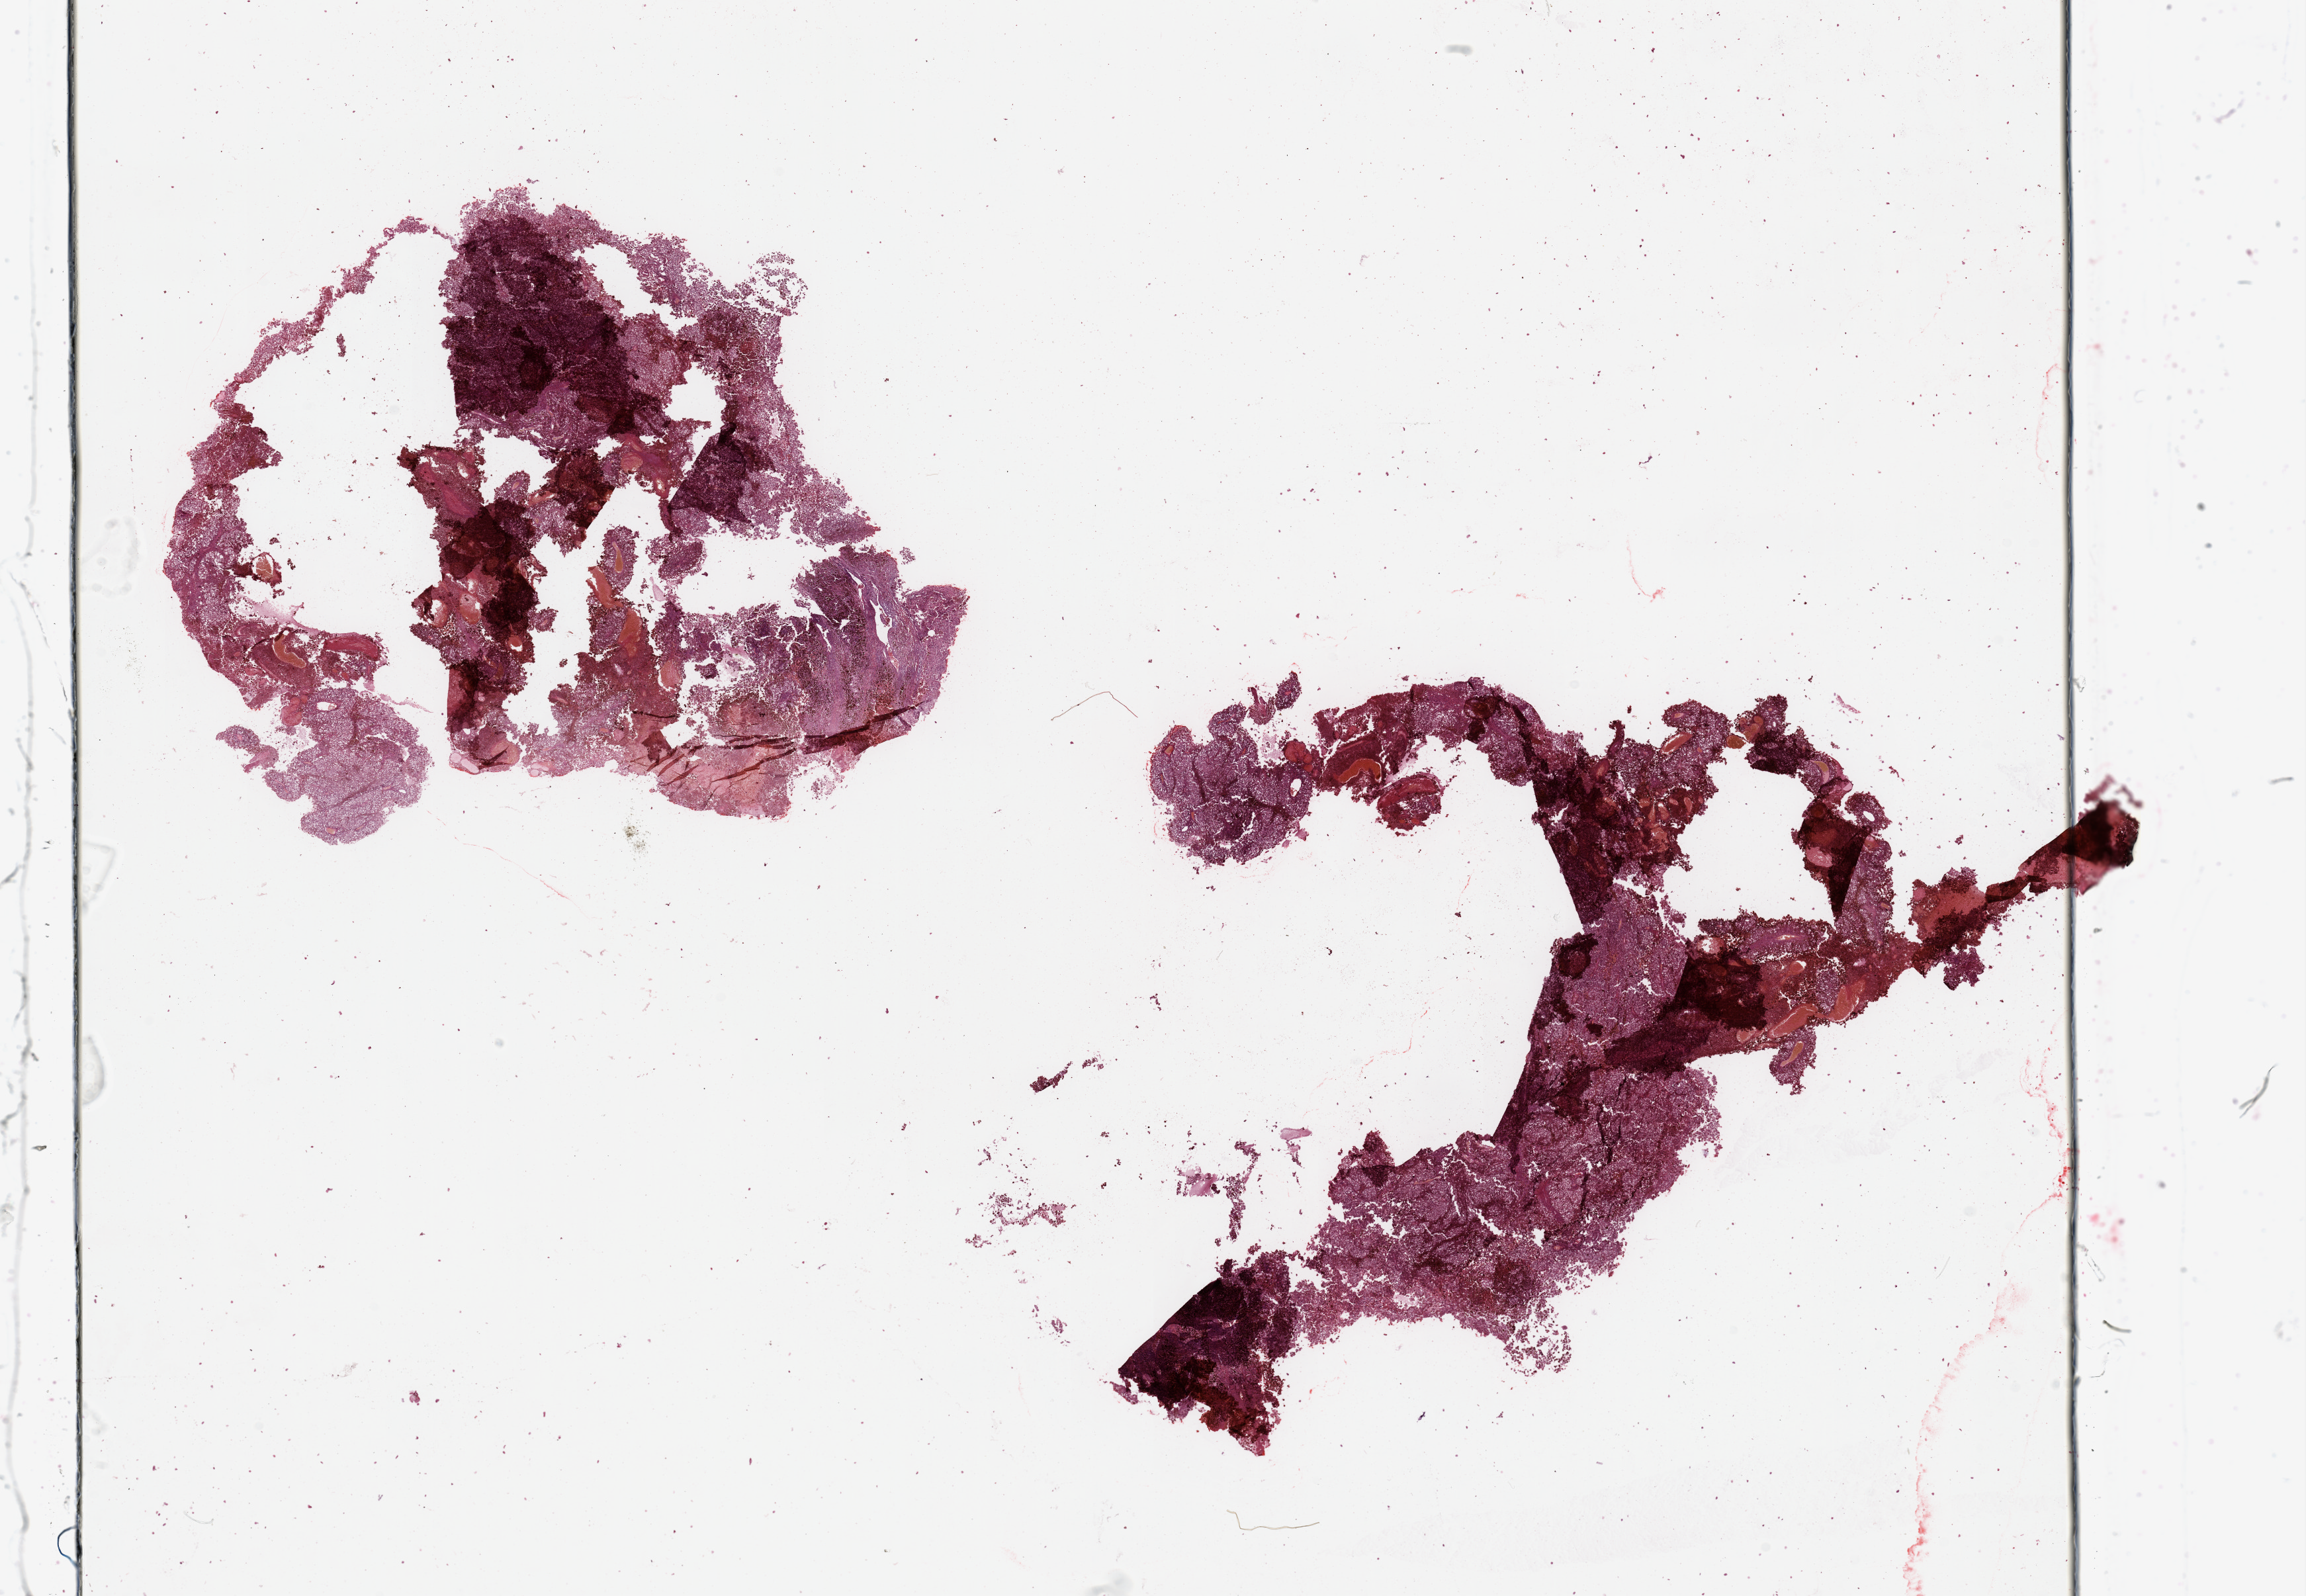
Whole-slide histology image, H&E-stained, a low-resolution overview of the entire scanned area, about 27.6 x 19.1 mm. Melanoma tumour tissue; sampled site not recorded. 67-year-old female patient.
Diagnosis: Malignant melanoma, NOS. Primary tumour site (as recorded): extremities. AJCC pathologic stage: IIB.